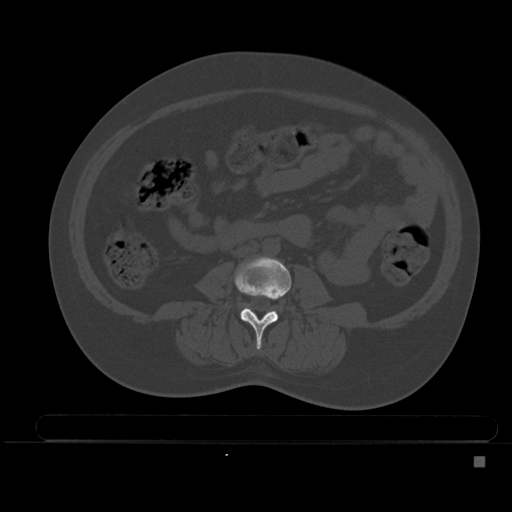
CT including the spine, one axial slice. Position 145 of 495 along the scan axis. Bone window (W 1800 / L 400 HU). 1.5 mm slice thickness. 512 × 512 image matrix, field of view 404 × 404 mm. Female patient, age 33 years. From the clinical record (not read from this slice): primary cancer: breast.
Outlined on this slice (semi-automatically segmented with operator editing):
- L3 vertebra: bounding box [x1, y1, x2, y2] px = [234, 256, 292, 349]